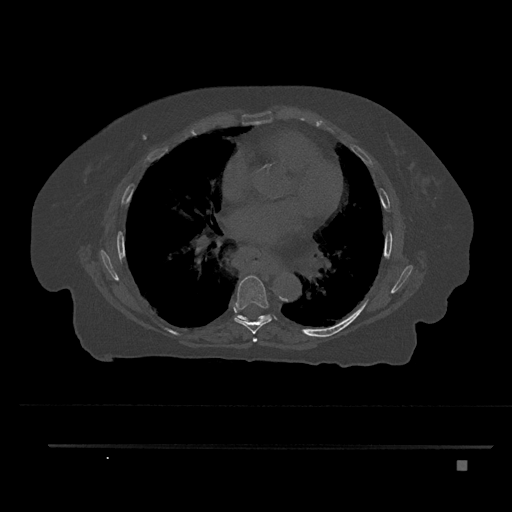
CT including the spine, one axial slice. Reconstruction kernel Br40s/3. 120 kVp. Bone window (W 1800 / L 400 HU). 0.5 mm slice thickness. 512 × 512 image matrix, field of view 437 × 437 mm. Female patient, age 76 years. Case-level facts recorded for this patient, not image findings: primary cancer: lung.
Annotated regions visible in this slice (semi-automatic segmentation, software-assisted and operator-edited):
- T6 vertebra: box from (x=253, y=337) to (x=257, y=343) px
- T7 vertebra: (x=234, y=275)–(x=272, y=334)
- T8 vertebra: (x=235, y=314)–(x=270, y=321)